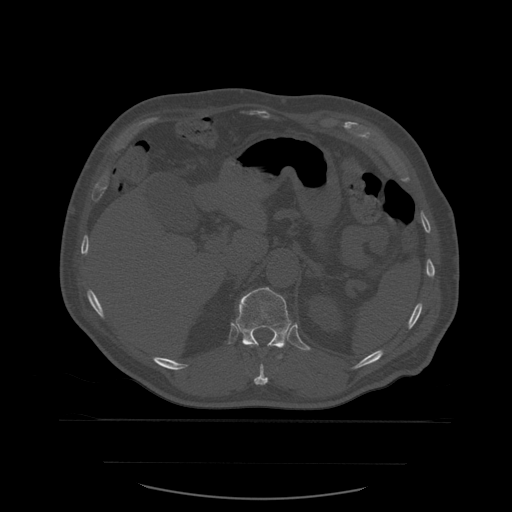
CT including the spine, one axial slice; slice 279 of 590 in the series (ordered by position); bone window (W 1800 / L 400 HU); 1.25 mm slice thickness; 512 × 512 image matrix, field of view 479 × 479 mm. Patient age 71 years. Case-level facts recorded for this patient, not image findings: primary cancer: lung.
Annotated regions visible in this slice (semi-automatically segmented with operator editing):
- T11 vertebra: box from (x=254, y=364) to (x=269, y=385) px
- T12 vertebra: (x=236, y=288)–(x=292, y=359)